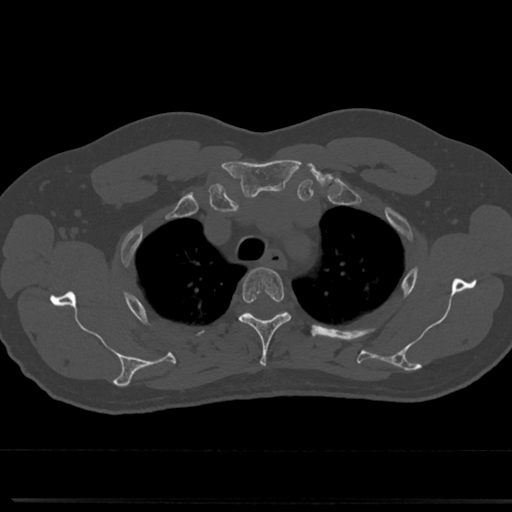
CT including the spine, one axial slice; slice 586 of 817 in the series (ordered by position); 120 kVp; bone window (W 1800 / L 400 HU); 0.5 mm slice thickness; 512 × 512 image matrix. Male patient, age 61 years. From the clinical record (not read from this slice): primary cancer: prostate.
Structures marked on this image (semi-automatic segmentation, software-assisted and operator-edited):
- T3 vertebra: bounding box [x1, y1, x2, y2] px = [239, 269, 291, 368]
- T4 vertebra: [242, 311, 306, 339]